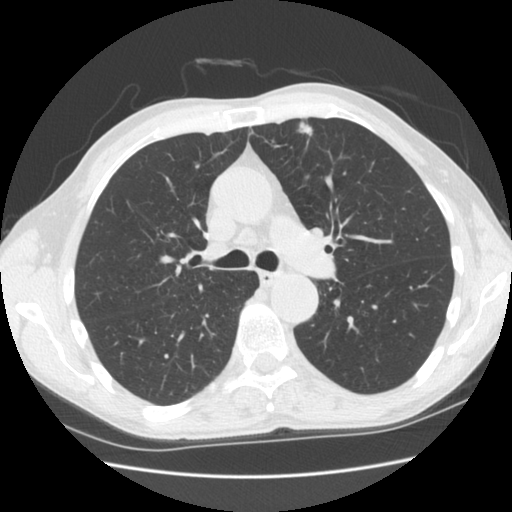
Low-dose screening chest CT, one axial slice; slice 109 of 169 in the series (ordered by position); 120 kVp; lung window (W 1500 / L -600 HU); 2.5 mm slice thickness; 512 × 512 image matrix.
Structures marked on this image (manually delineated by an expert):
- lesion 1 (tumor, upper lobe of left lung): box from (x=296, y=122) to (x=314, y=136) px